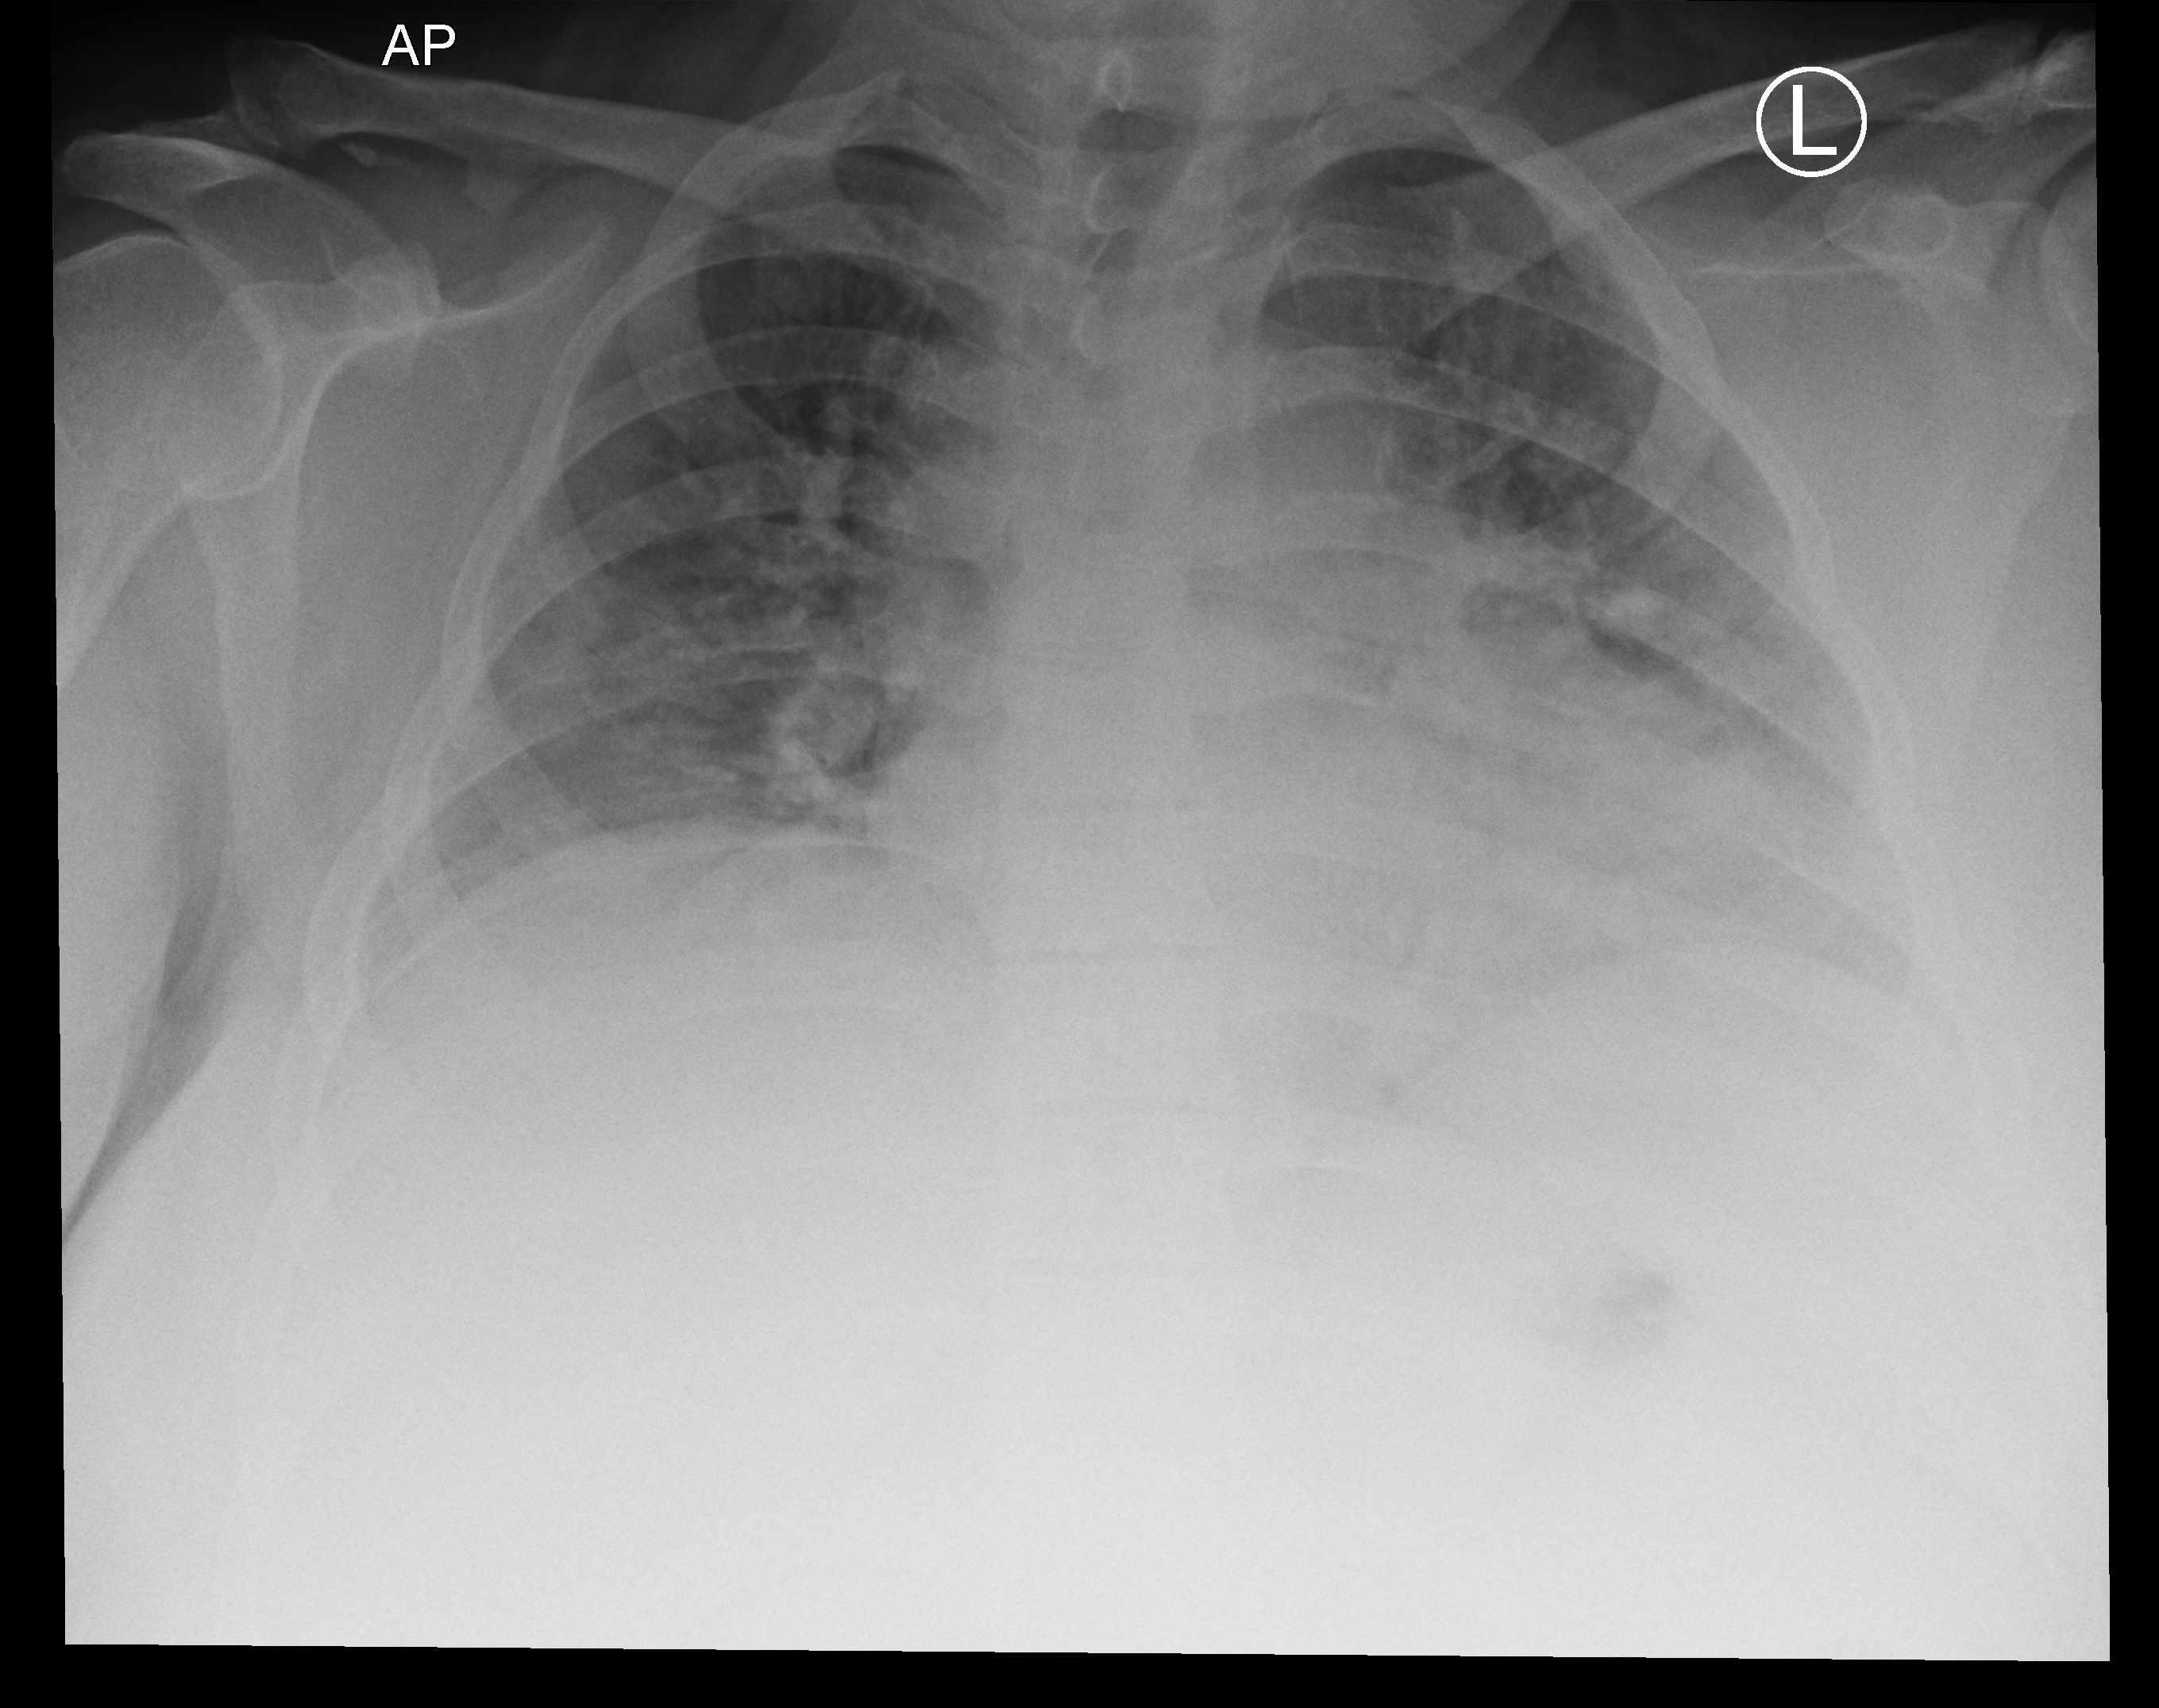
Portable chest radiograph, anteroposterior (AP) projection. Patient hospitalised with COVID-19; female, aged 18–59 years.
Admission-level facts for this patient (not findings on this image; timing relative to this image not recorded):
- mechanically ventilated during this hospital stay: yes